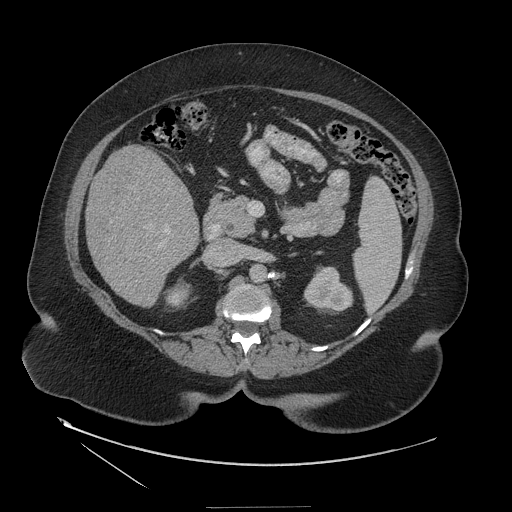
Contrast-enhanced abdominal CT (liver protocol), one axial slice. Position 58 of 127 along the scan axis. 140 kVp. Soft-tissue window (W 400 / L 40 HU). 512 × 512 image matrix, field of view 480 × 480 mm. From the clinical record (not read from this slice): diagnosis: hepatocellular carcinoma (patient treated with transarterial chemoembolisation; whether this scan precedes or follows treatment is not stated here); TNM stage (as recorded): Stage-II; Child-Pugh class: A; tumour differentiation: well differentiated; tumour nodularity: multinodular.
Outlined on this slice (semi-automatically segmented with operator editing):
- liver parenchyma outside the tumour (the mass and vessels are separate outlines, so this box may not span the whole liver): bounding box [x1, y1, x2, y2] px = [86, 145, 198, 306]